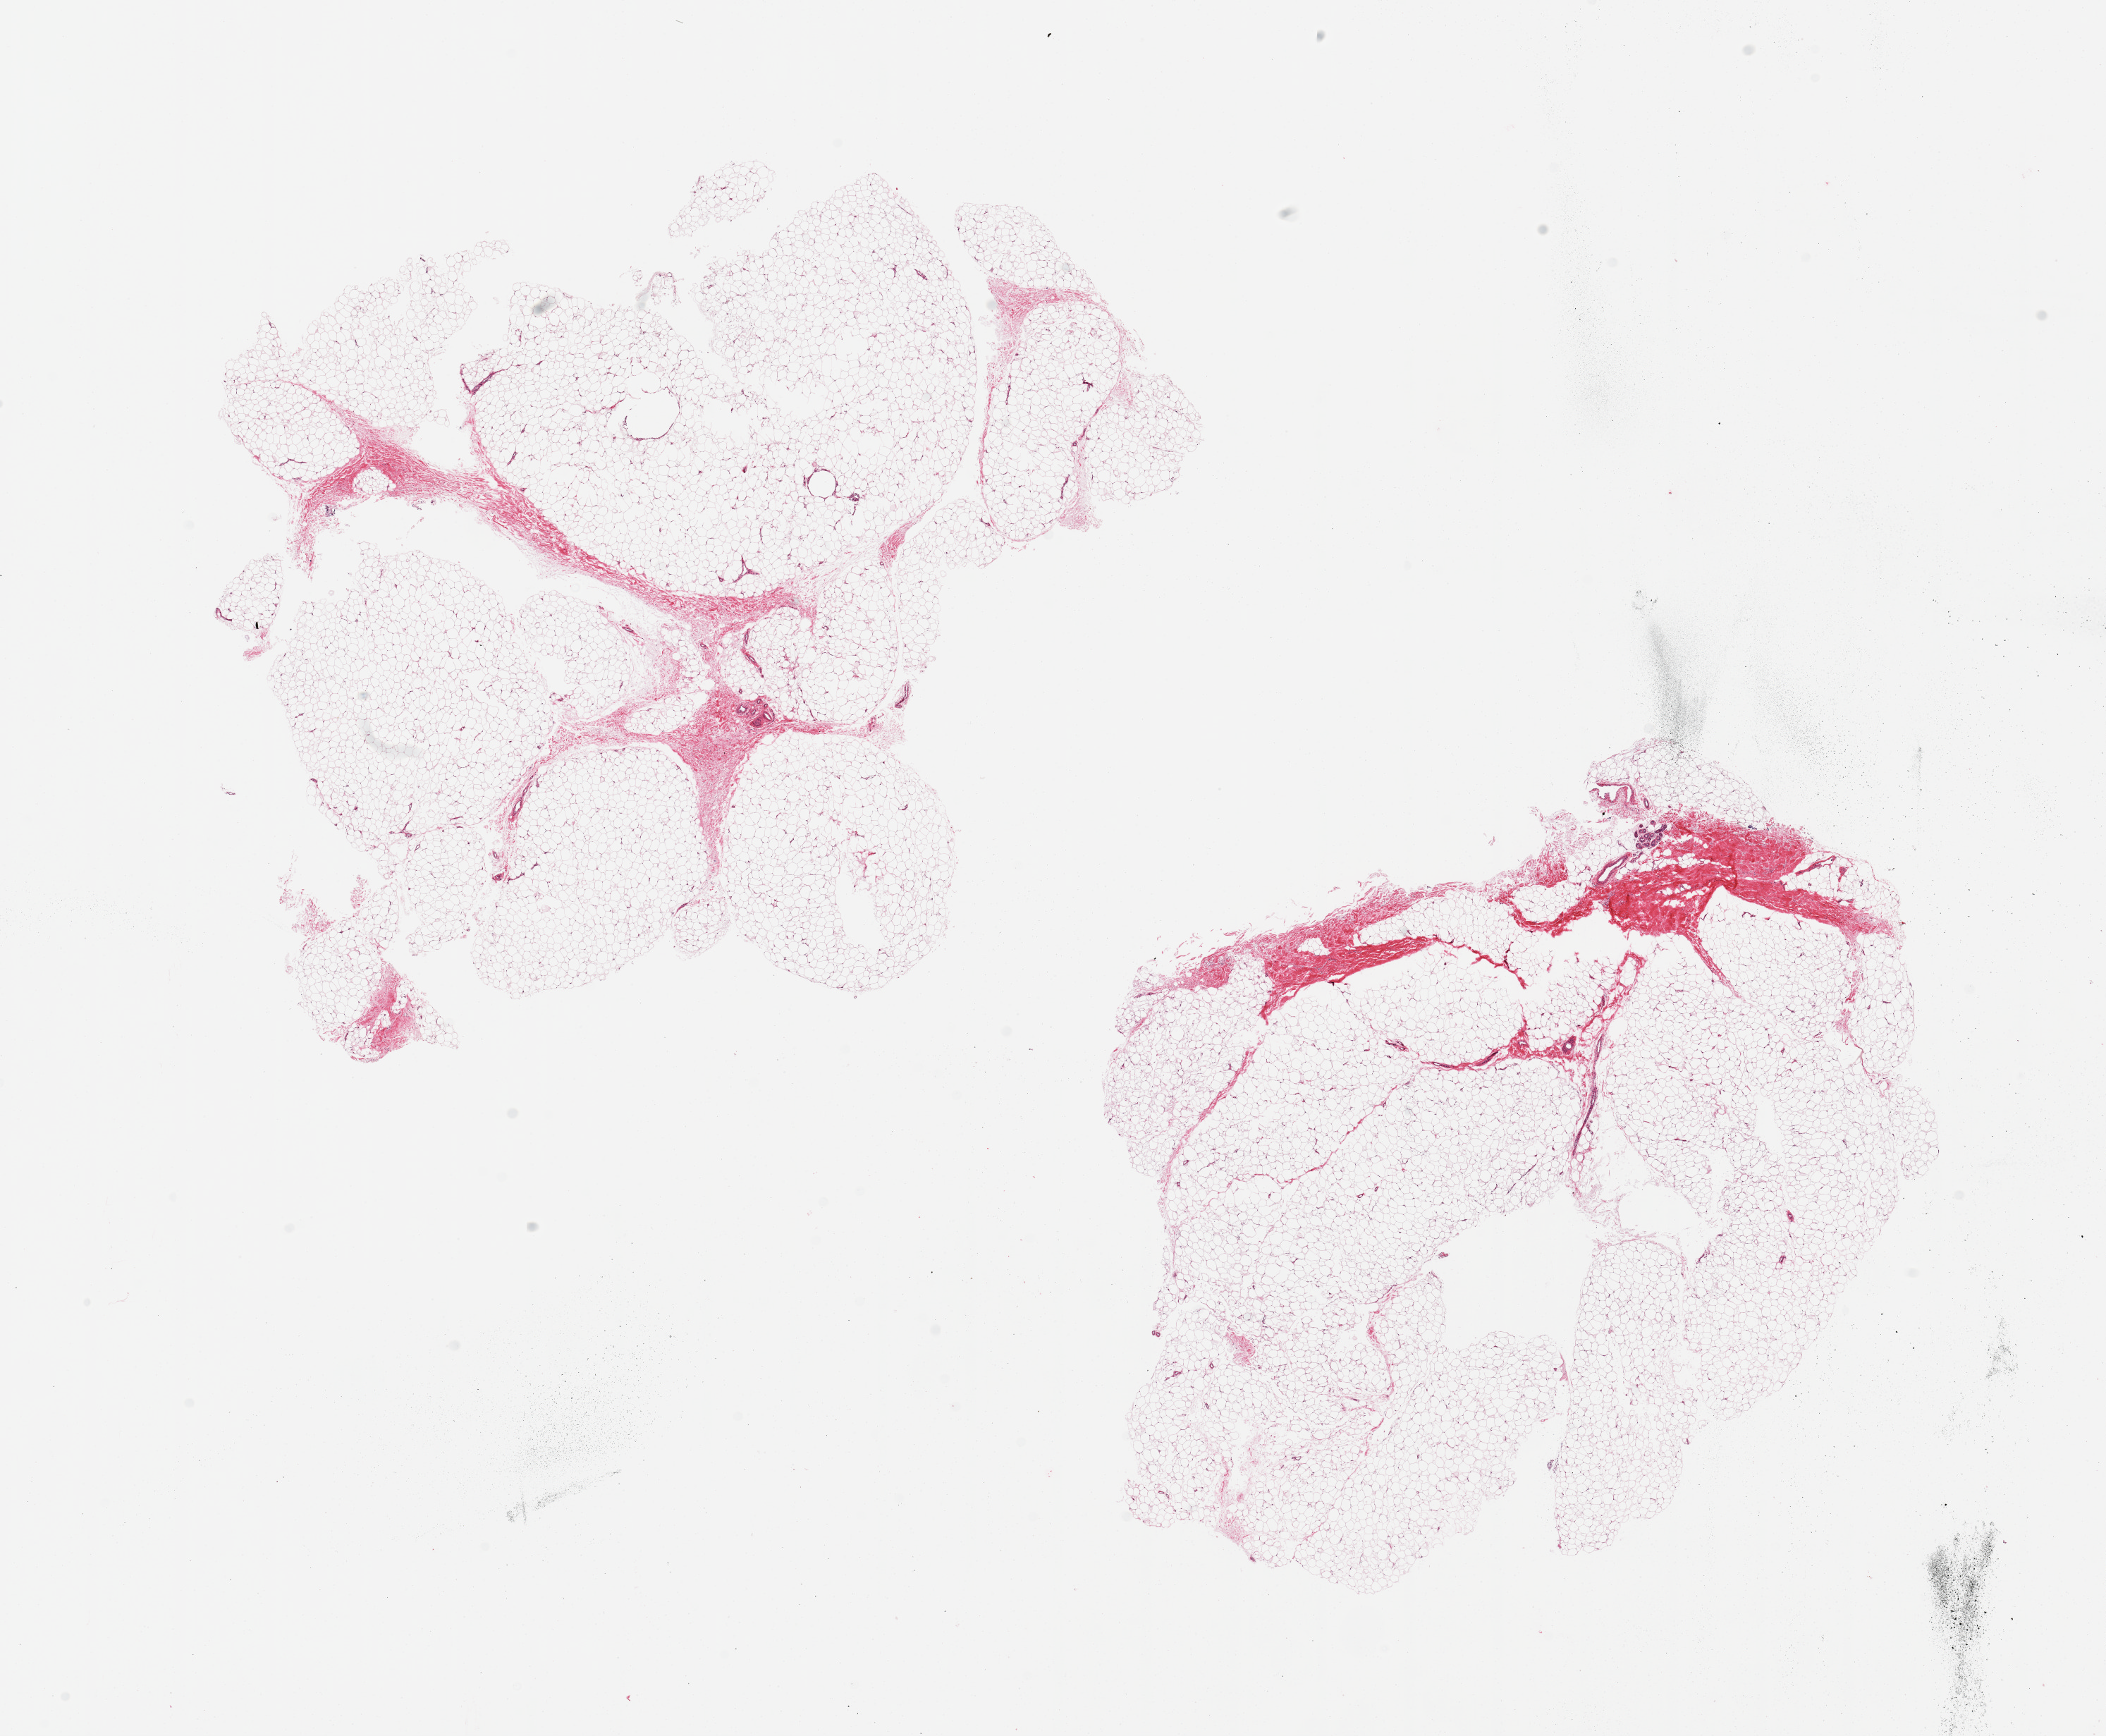
Whole-slide image, hematoxylin and eosin (H&E) stain, whole scanned area (about 23.6 x 19.5 mm) shown as a low-resolution overview; PAXgene-fixed paraffin-embedded (PFPE) section; sampled site (target tissue): adipose tissue; tissue donor sample. Donor sex: female.
- pathologist's review note for this sample: 2 pieces; fat with <10% fibrovascular tissue/collagen with focus of sweat glands